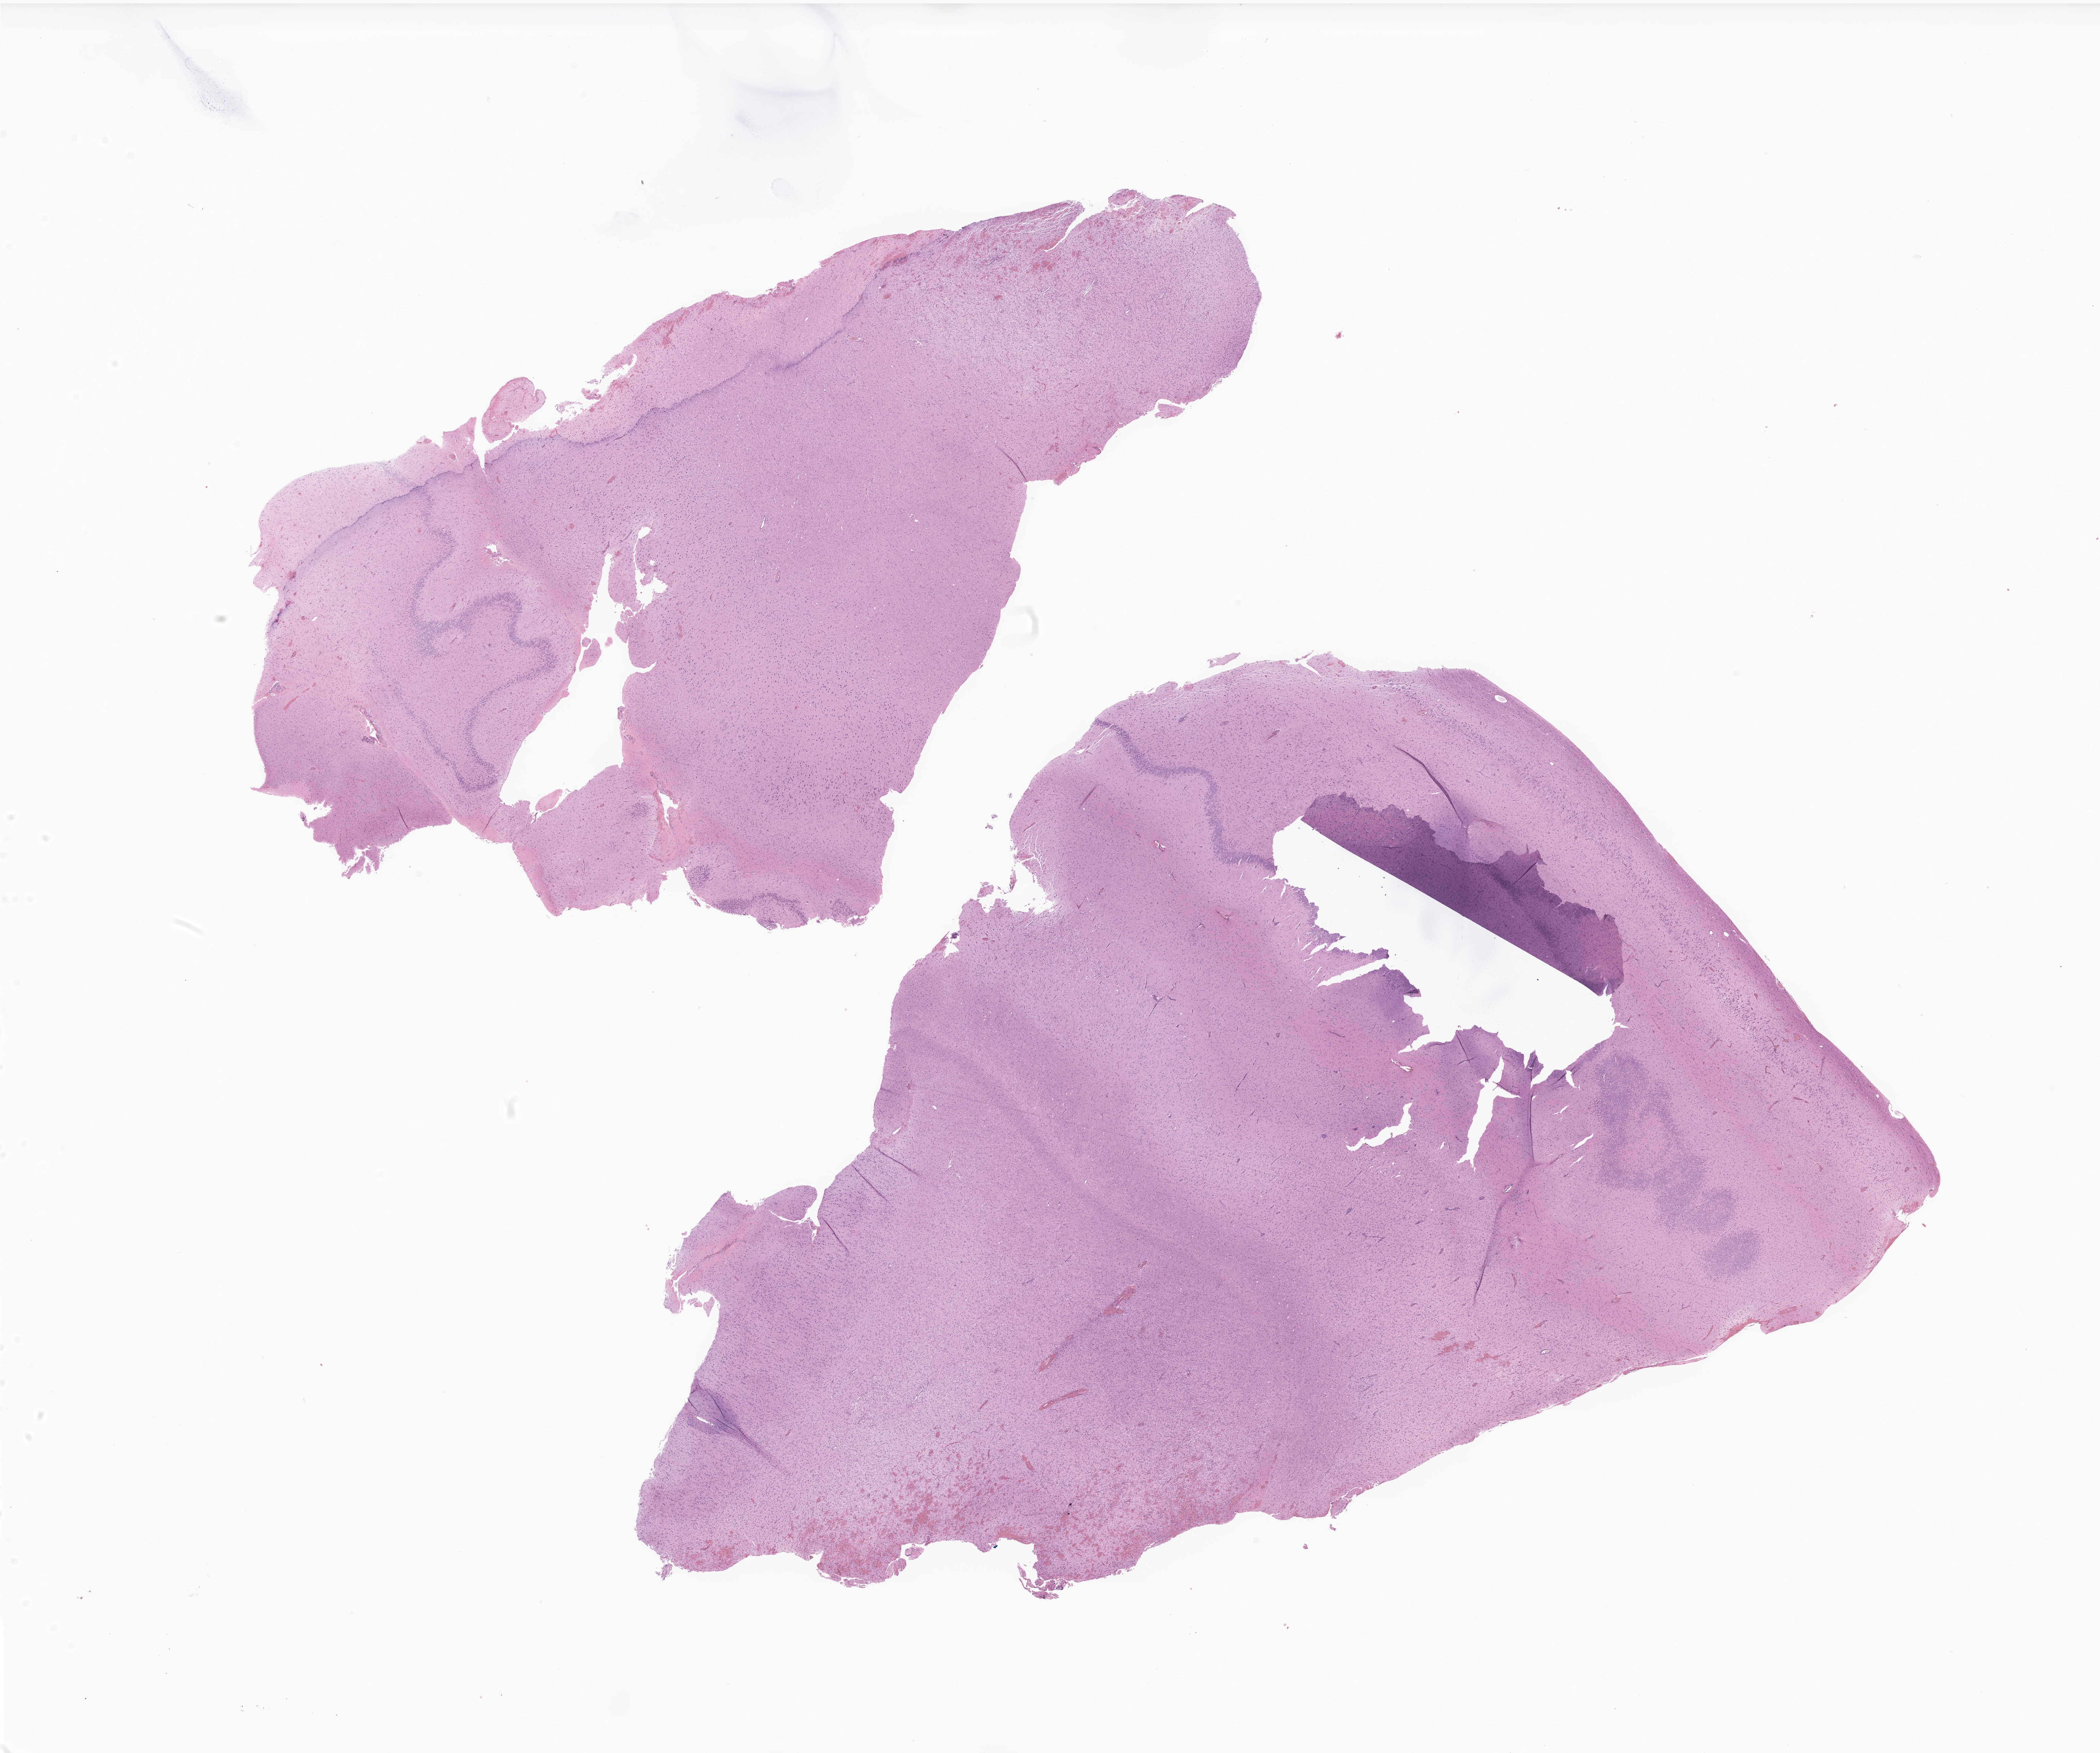
Digitized haematoxylin and eosin-stained section of tumor tissue from the brain — whole scanned area (about 26.0 x 21.7 mm) shown as a low-resolution overview; FFPE section. Male patient, age 583 days.
Diagnosis: Astrocytoma, NOS.